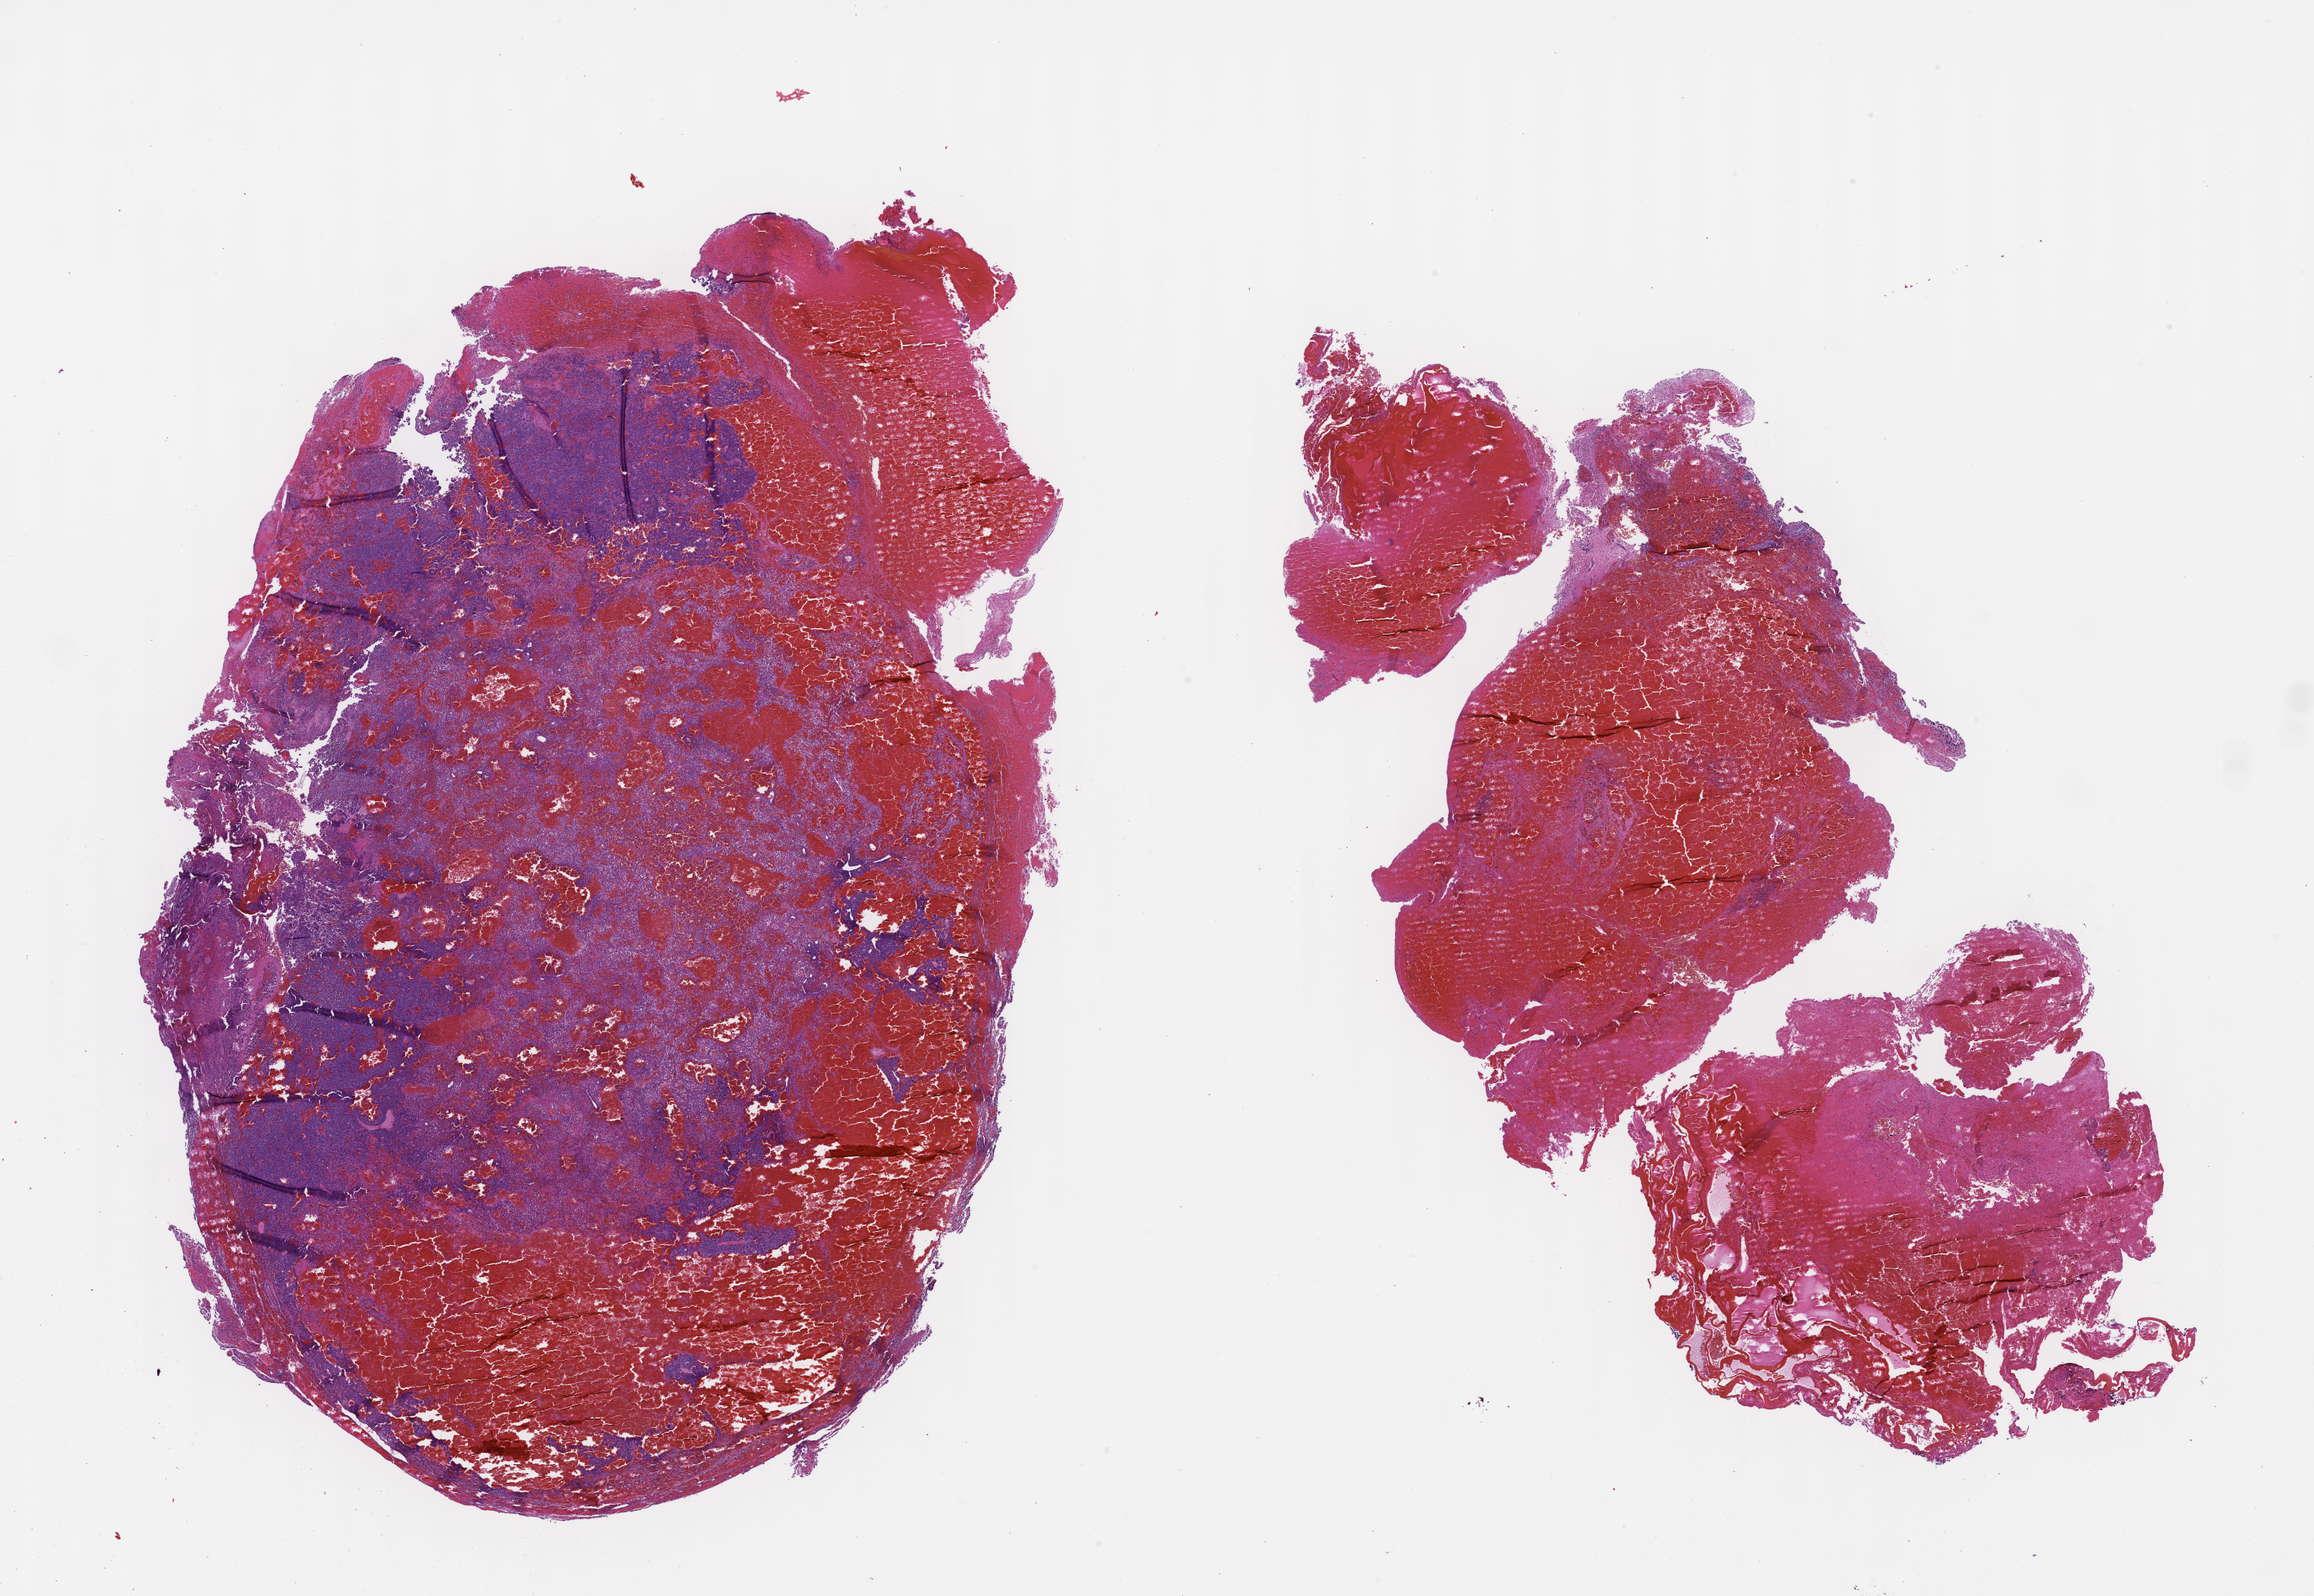
Hematoxylin and eosin (H&E) whole-slide image — shown as a low-resolution overview of the whole scanned area (about 24.1 x 16.6 mm), formalin-fixed paraffin-embedded section, specimen time point: archival tissue. Patient sex: female.
This section: metastatic tumor tissue. Patient diagnosis (primary): Melanoma.